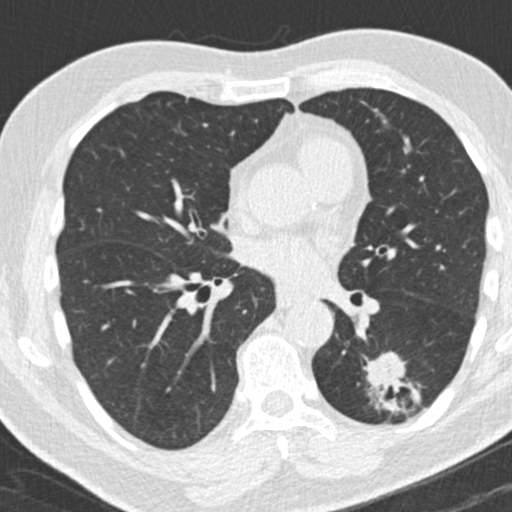
Chest CT (low-dose screening protocol), one axial image. Third annual screen. Lung window (W 1500 / L -600 HU). 2 mm slice thickness. Slice 84 of 180 in the series. 512 × 512 image matrix. Male, age 66 years at enrolment.
Lesion marked by an expert reader, box from (x=356, y=352) to (x=425, y=427) px. Screening reader's record for this exam (one nodule recorded; not confirmed to be the boxed lesion): non-calcified nodule or mass ≥4 mm, left lower lobe, 31 × 24 mm, spiculated (stellate) margins, pre-existing on the prior screen: yes; interval growth: yes.